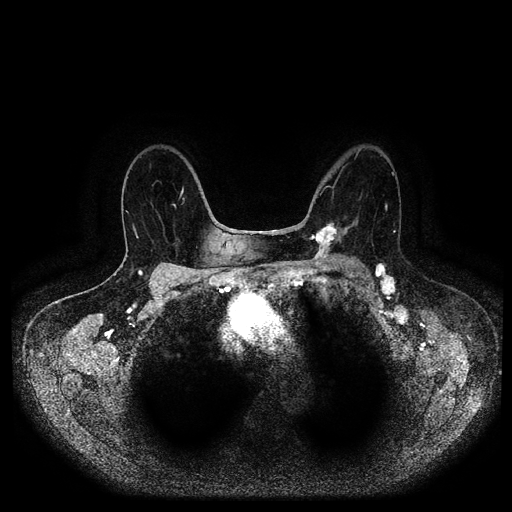
Breast MRI (dynamic contrast-enhanced, multi-phase), one axial slice. Slice 63 of 116 in the series (ordered by position). Dynamic contrast-enhanced series, time point 2 of 5 at this slice position (early post-contrast). 1.5 T. TE 2.6 ms, TR 5.2 ms. 2 mm slice thickness. 512 × 512 image matrix, field of view 380 × 380 mm. Patient: female, 69 years.
Structures marked on this image (semi-automatic segmentation, software-assisted and operator-edited):
- breast lesion (labelled 'tumour' in the annotation; benign lesions carry a separate 'benign' label): bounding box [x1, y1, x2, y2] px = [308, 222, 343, 261]